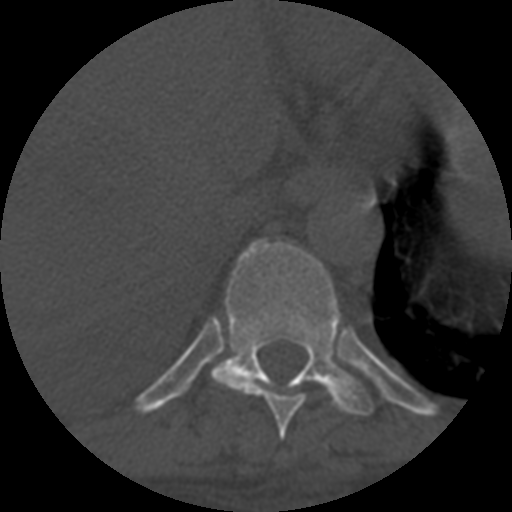
CT including the spine, one axial slice. Slice 365 of 708 in the series (ordered by position). One of 3 acquisitions stored at this slice position. Bone window (W 1800 / L 400 HU). 1.25 mm slice thickness. 512 × 512 image matrix, field of view 160 × 160 mm. Patient age 55 years. Case-level facts recorded for this patient, not image findings: primary cancer: colon; vertebrae with lytic lesions (as recorded): T12, L1, L5.
Annotated regions visible in this slice (semi-automatically segmented with operator editing):
- T10 vertebra: bounding box [x1, y1, x2, y2] px = [213, 241, 375, 416]
- T9 vertebra: [214, 372, 306, 440]